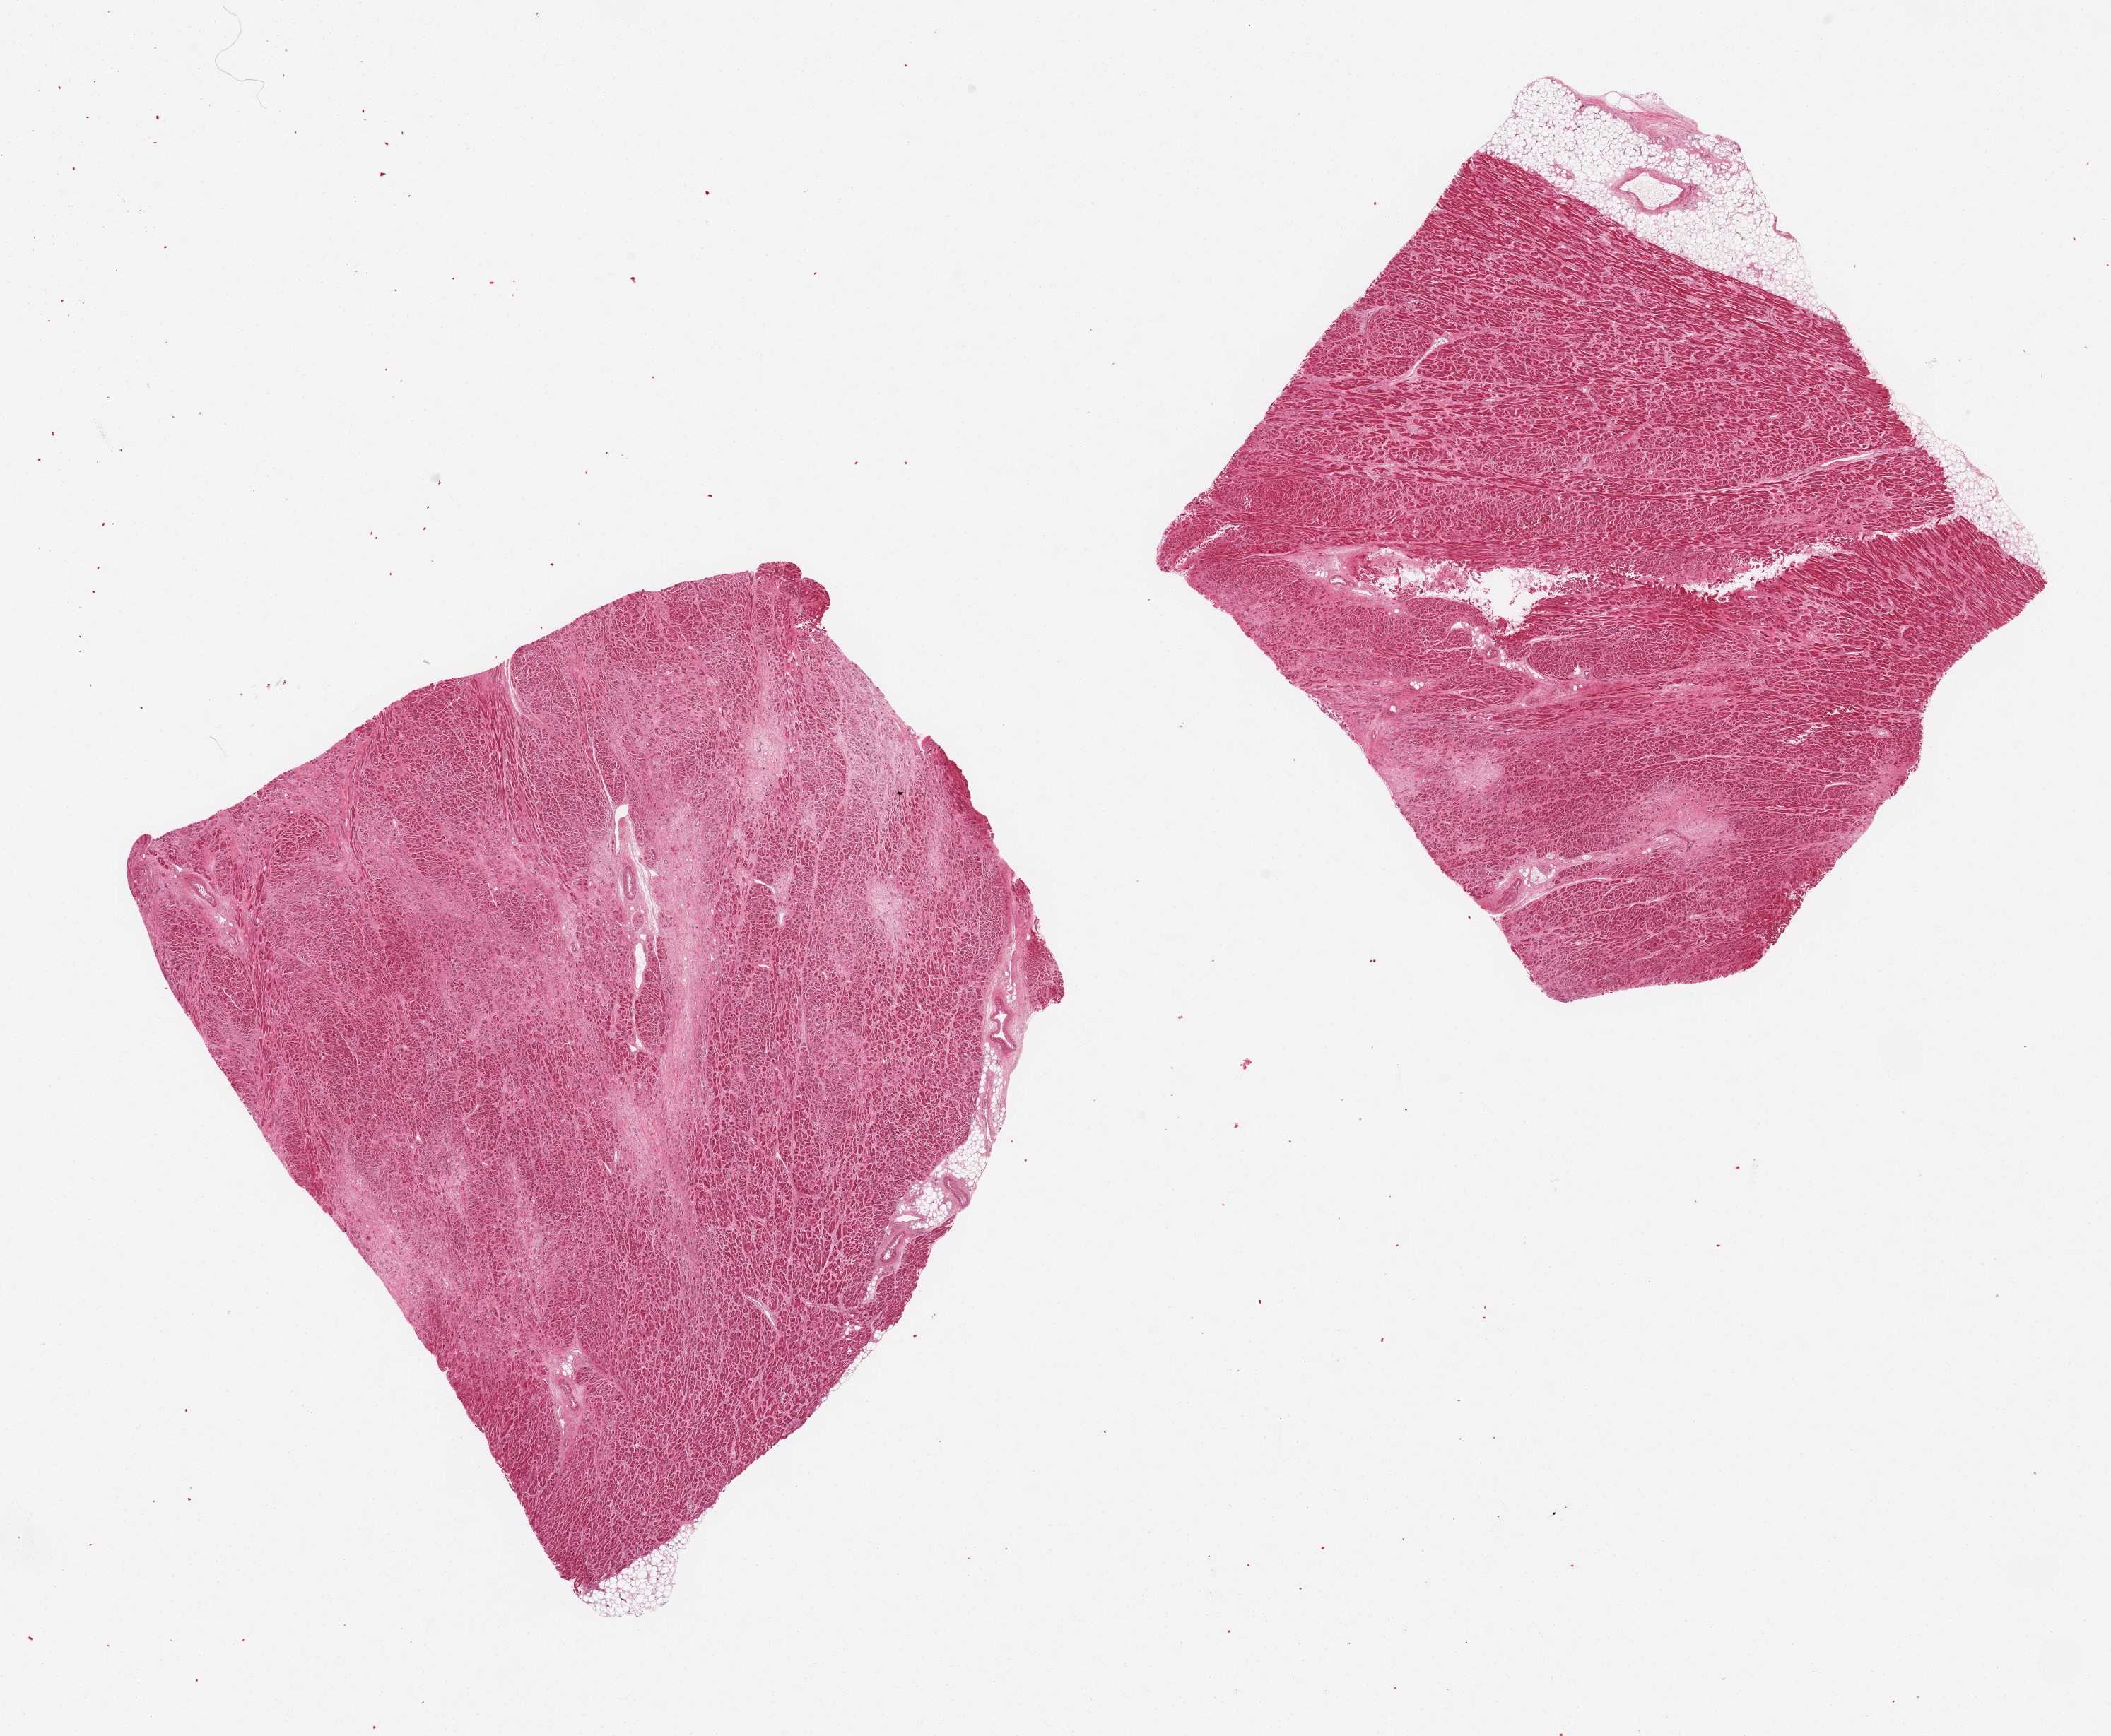
H&E whole-slide image — low-resolution overview of the scanned area, about 23.6 x 19.4 mm, PAXgene-fixed paraffin-embedded (PFPE) section, target tissue: heart, donor tissue sample.
Review note (as recorded): 2 pieces, extensive ischemic damage, with remote infarct (foci) and subacute ischemic damage.